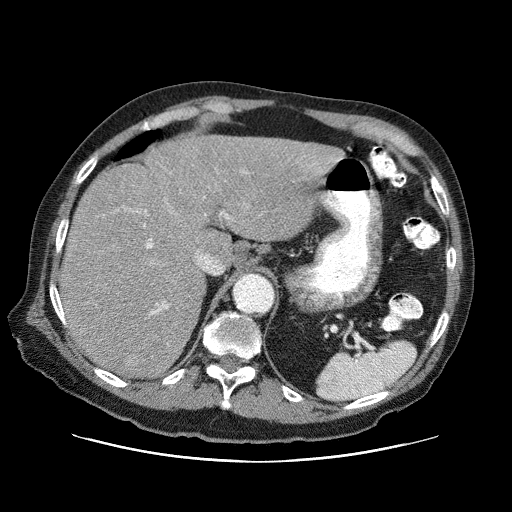
Contrast-enhanced abdominal CT (liver protocol), one axial slice. Position 52 of 87 along the scan axis. One of 3 acquisitions stored at this slice position. Soft-tissue window (W 400 / L 40 HU). 2.5 mm slice thickness. 512 × 512 image matrix, field of view 400 × 400 mm. From the clinical record (not read from this slice): diagnosis: hepatocellular carcinoma (patient treated with transarterial chemoembolisation; whether this scan precedes or follows treatment is not stated here); TNM stage (as recorded): Stage-IIIA; Child-Pugh class: A; tumour differentiation: well differentiated; tumour size: 6 cm.
Outlined on this slice (semi-automatically segmented with operator editing):
- abdominal aorta: bounding box <235,273,273,313> (left, top, right, bottom; pixels)
- liver parenchyma outside the tumour (the mass and vessels are separate outlines, so this box may not span the whole liver): <60,136,343,378>
- liver vessels: <138,159,340,314>